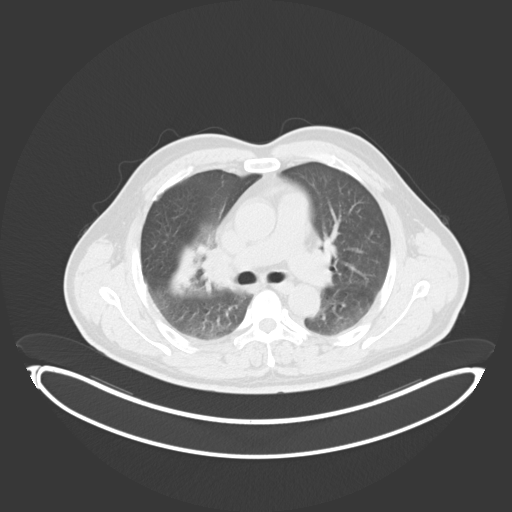
Chest CT, one axial slice; slice 213 of 284 in the series (ordered by position); 120 kVp; lung window (W 1500 / L -600 HU); 512 × 512 image matrix, field of view 500 × 500 mm. Patient: male, 55 years. From the clinical record (not read from this slice): clinical TNM (as recorded): T3 N2 M1.
Structures marked on this image (bounding box drawn by a radiologist):
- lung tumour (recorded histology: adenocarcinoma): box from (x=167, y=240) to (x=201, y=296) px